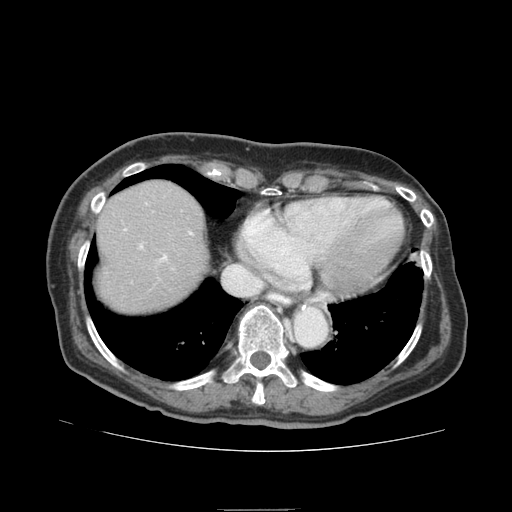
Contrast-enhanced abdominal CT (liver protocol), one axial slice; position 73 of 95 along the scan axis; 140 kVp; soft-tissue window (W 400 / L 40 HU); 2.5 mm slice thickness; 512 × 512 image matrix, field of view 360 × 360 mm. From the clinical record (not read from this slice): diagnosis: hepatocellular carcinoma (patient treated with transarterial chemoembolisation; whether this scan precedes or follows treatment is not stated here); TNM stage (as recorded): Stage-IVA; Child-Pugh class: B; tumour differentiation: moderately differentiated.
Annotated regions visible in this slice (semi-automatically segmented with operator editing):
- abdominal aorta: bounding box <295,307,327,346> (left, top, right, bottom; pixels)
- liver parenchyma outside the tumour (the mass and vessels are separate outlines, so this box may not span the whole liver): <96,180,208,312>
- liver vessels: <124,229,193,262>